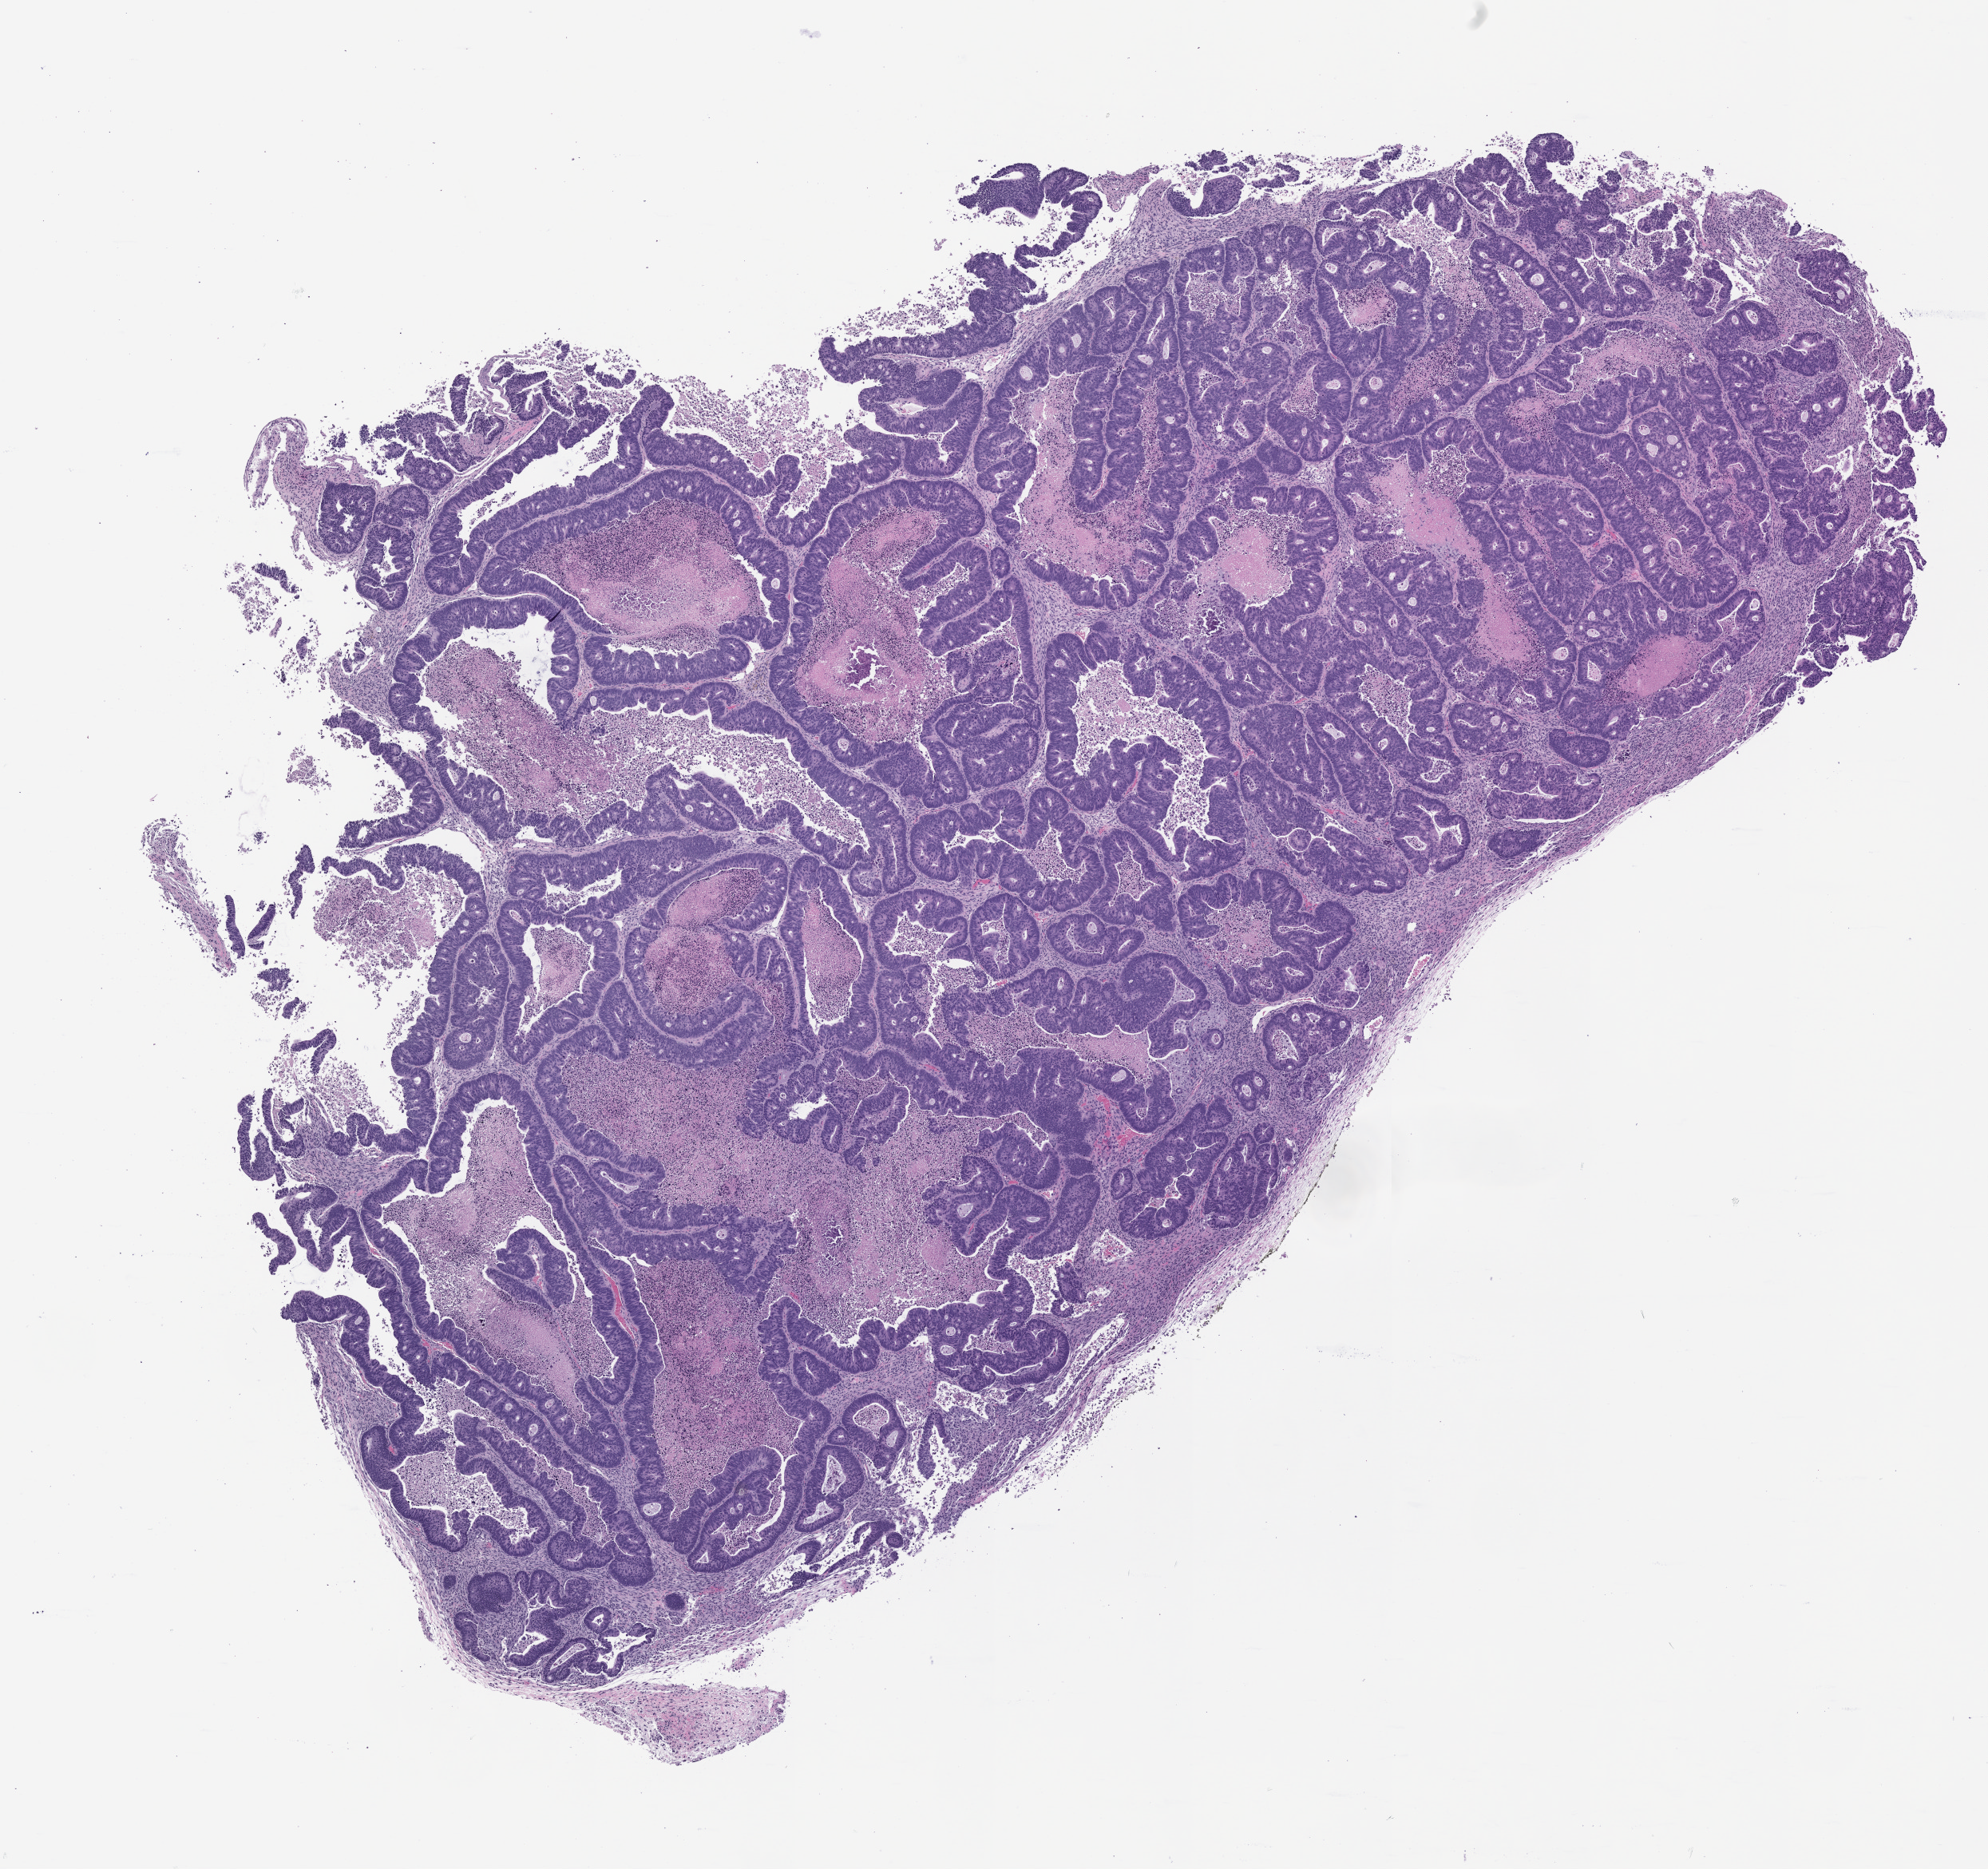
Haematoxylin and eosin whole-slide image of a patient-derived xenograft (PDX) tumor grown in a mouse, passage 0, shown as a low-resolution overview of the whole scanned area (about 10.0 x 9.4 mm); formalin-fixed paraffin-embedded section; tumor site category: colon.
- originating patient diagnosis: Colon Adenocarcinoma